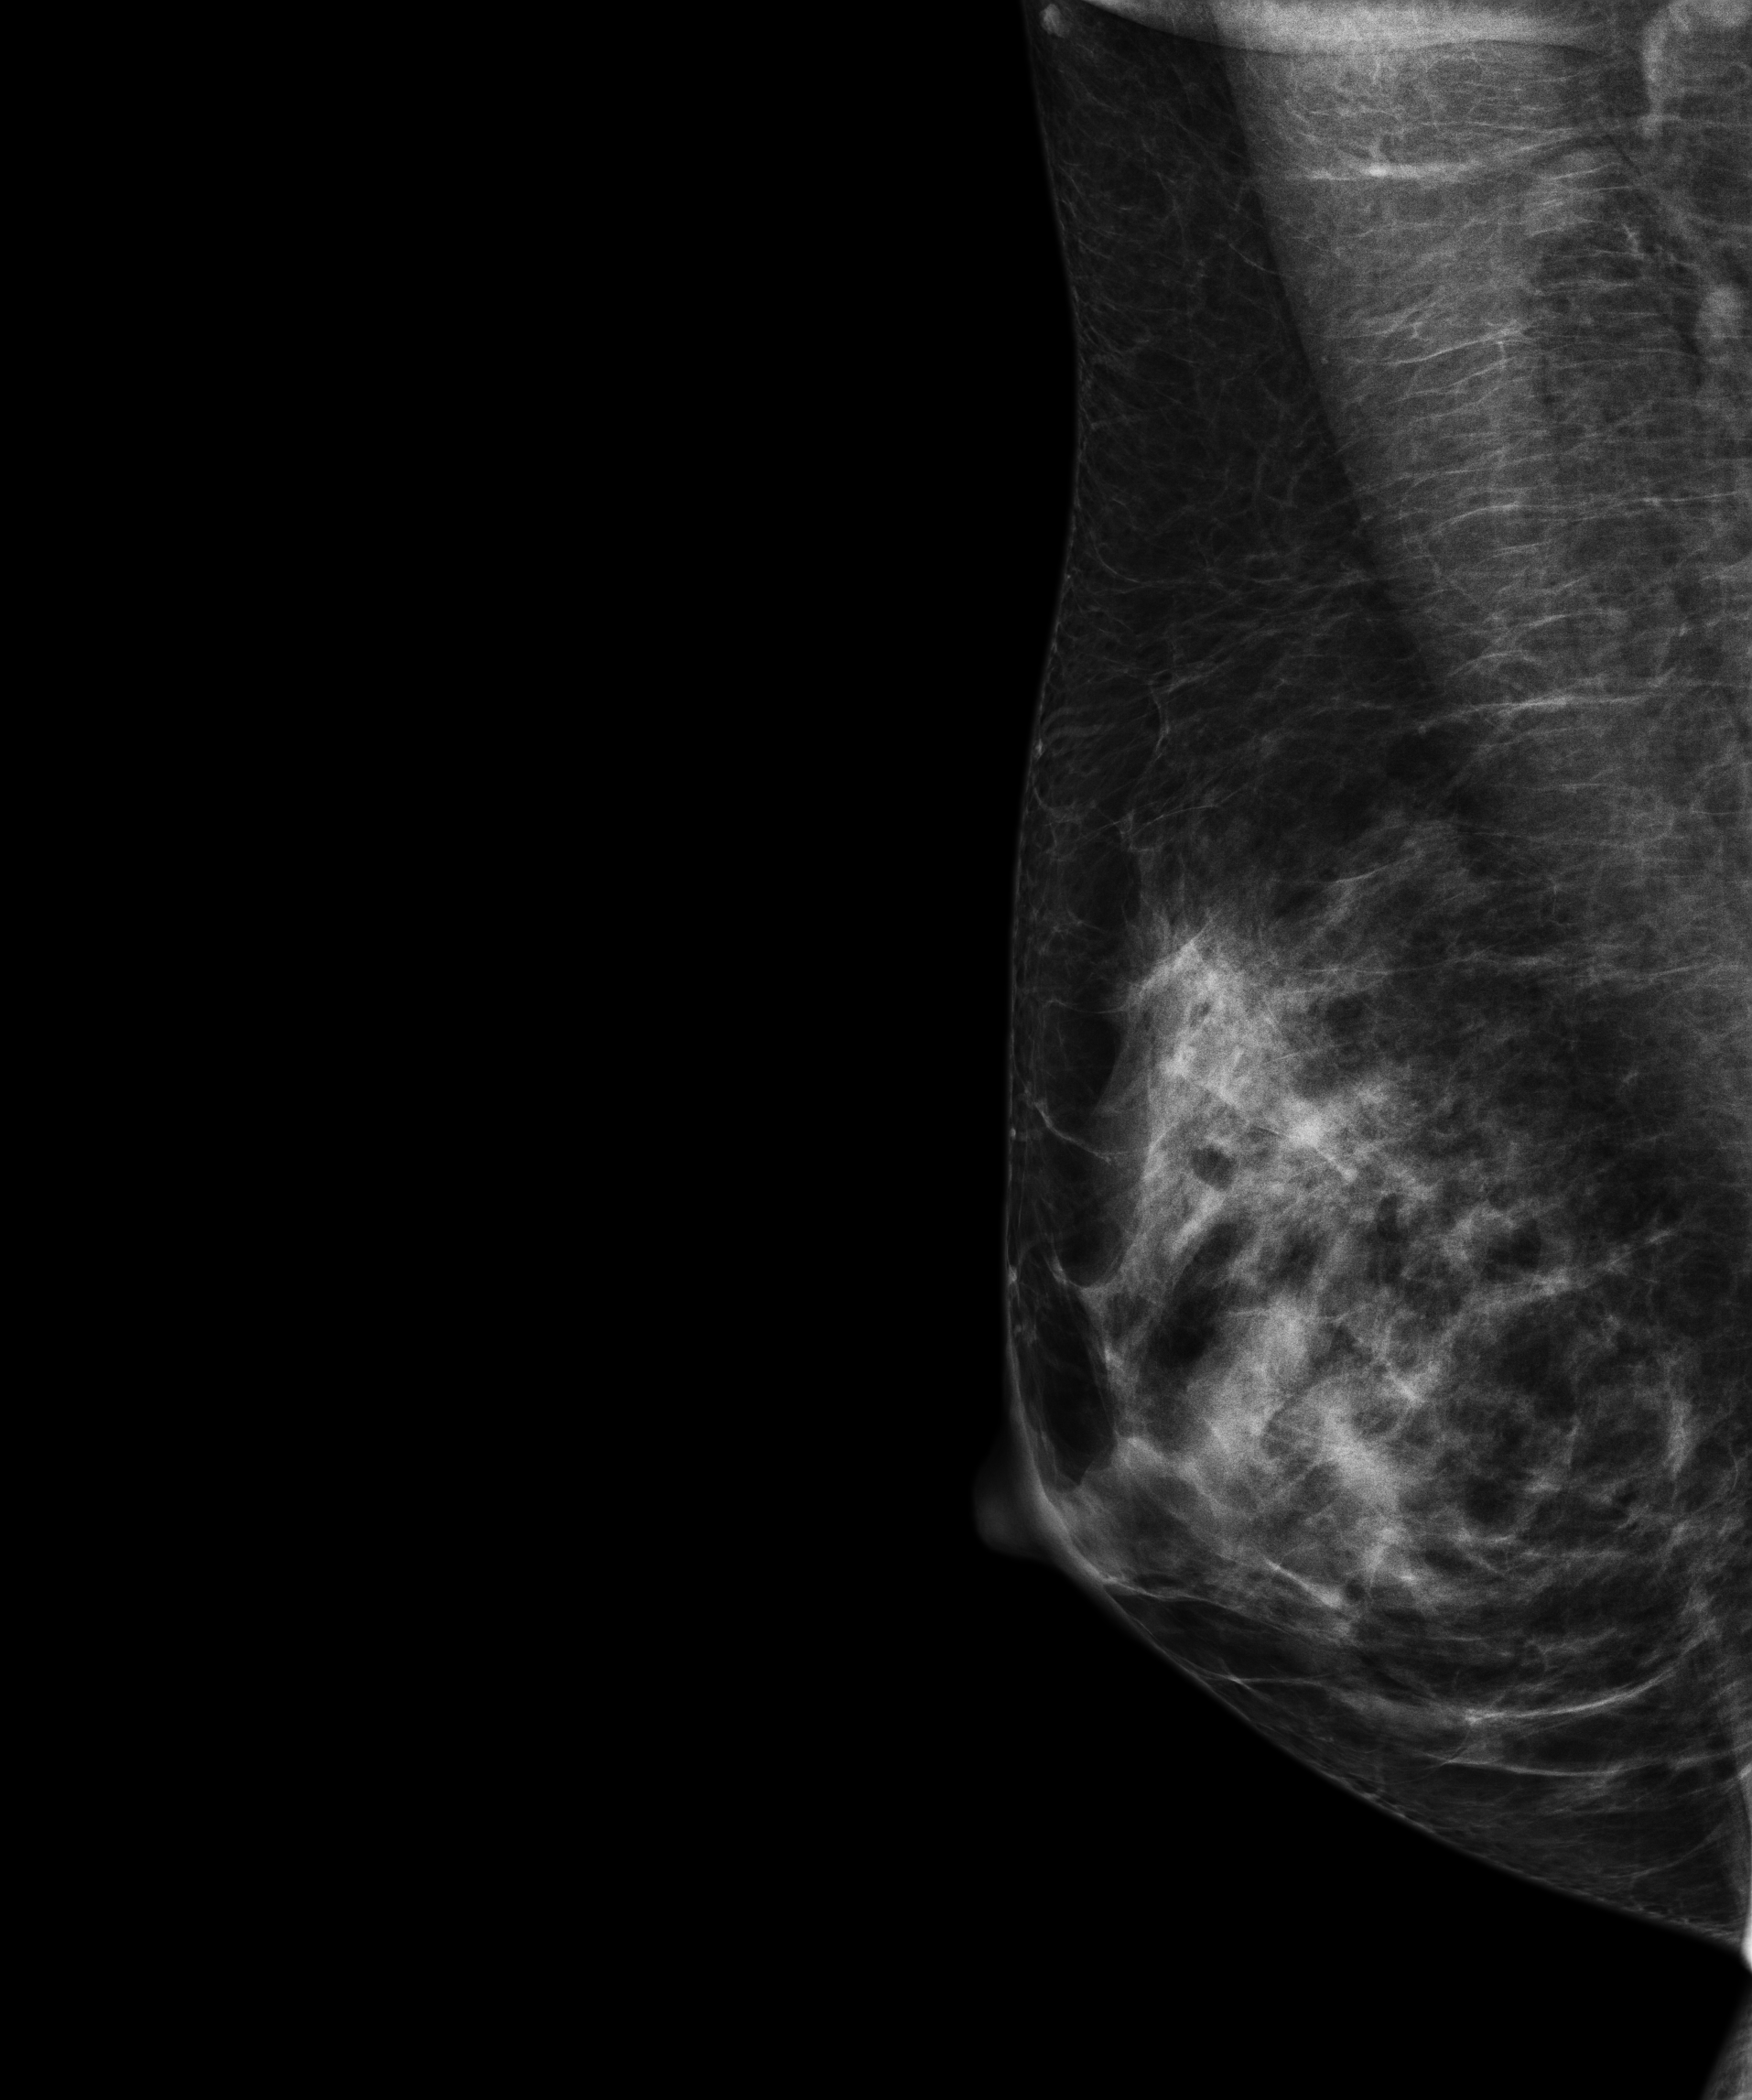
Full-field digital mammogram (FFDM); right breast; MLO view; screening examination; system: Senographe Essential ADS_56.21.3. Female patient, age 42 years.
BI-RADS breast density category at the screening exam (both breasts, scale 1–4): 3. Final BI-RADS assessment for this screening round (tomosynthesis exam, both breasts): category 1. Recall: no recall after this screen.